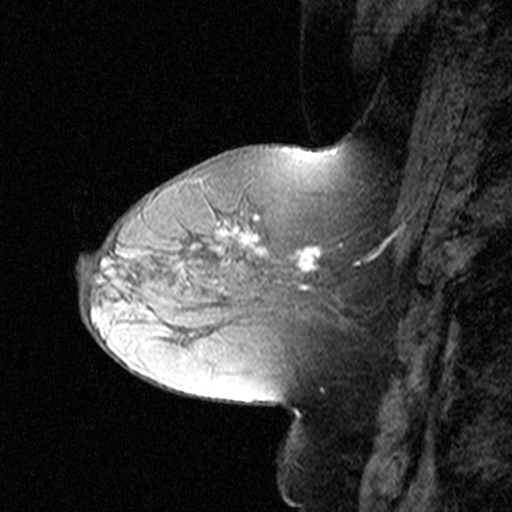
Breast MRI (dynamic contrast-enhanced), one sagittal slice. Position 17 of 44 along the scan axis. Dynamic contrast-enhanced study with each time point stored as its own series, time point 2 of 3 at this slice position (early post-contrast, ordered by acquisition time). 1.5 T. TE 4.5 ms, TR 11 ms. 3 mm slice thickness. 512 × 512 image matrix, field of view 200 × 200 mm. Patient: female, 50 years. Case-level facts recorded for this patient, not image findings: setting: breast cancer imaged before/during neoadjuvant chemotherapy; receptor status: HR-positive, HER2-negative.
Outlined on this slice (semi-automatic segmentation, software-assisted and operator-edited):
- analysis volume of interest (the breast-tissue region the enhancement analysis was run in; not a lesion): bounding box (x1, y1, x2, y2) in pixels: (180, 198, 324, 311)
- tumour enhancement mask (voxels above the 90 % enhancement threshold inside the analysis volume of interest): (216, 227, 322, 271)